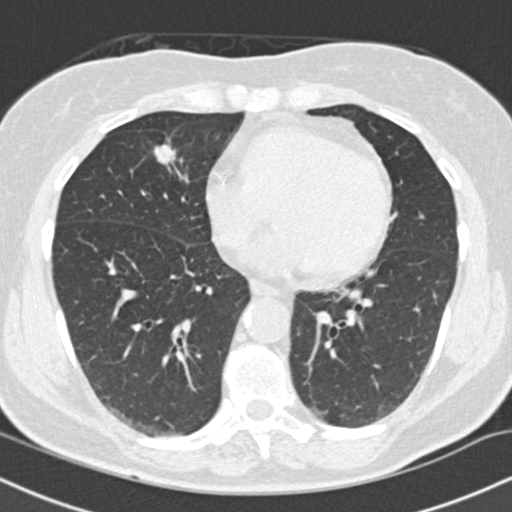
Axial slice from a low-dose chest CT screening exam, baseline annual screen, lung window (W 1500 / L -600 HU), 2 mm slice thickness, slice 86 of 145 in the series. Female, age 66 years at enrolment. Current smoker at enrolment.
• Expert-annotated lung lesion, bounding box [x1, y1, x2, y2] px = [140, 133, 183, 171].
• Reader record for this screening exam (exam-level; its link to the box is not recorded): non-calcified nodule or mass ≥4 mm, right lower lobe, 10 × 8 mm, smooth margins, soft tissue attenuation.
• Lung cancer was diagnosed 96 days after this screen: squamous cell carcinoma, keratinizing, NOS, right upper lobe, right middle lobe, poorly differentiated (G3), stage IA (AJCC 6th edition), 14 mm at pathology.